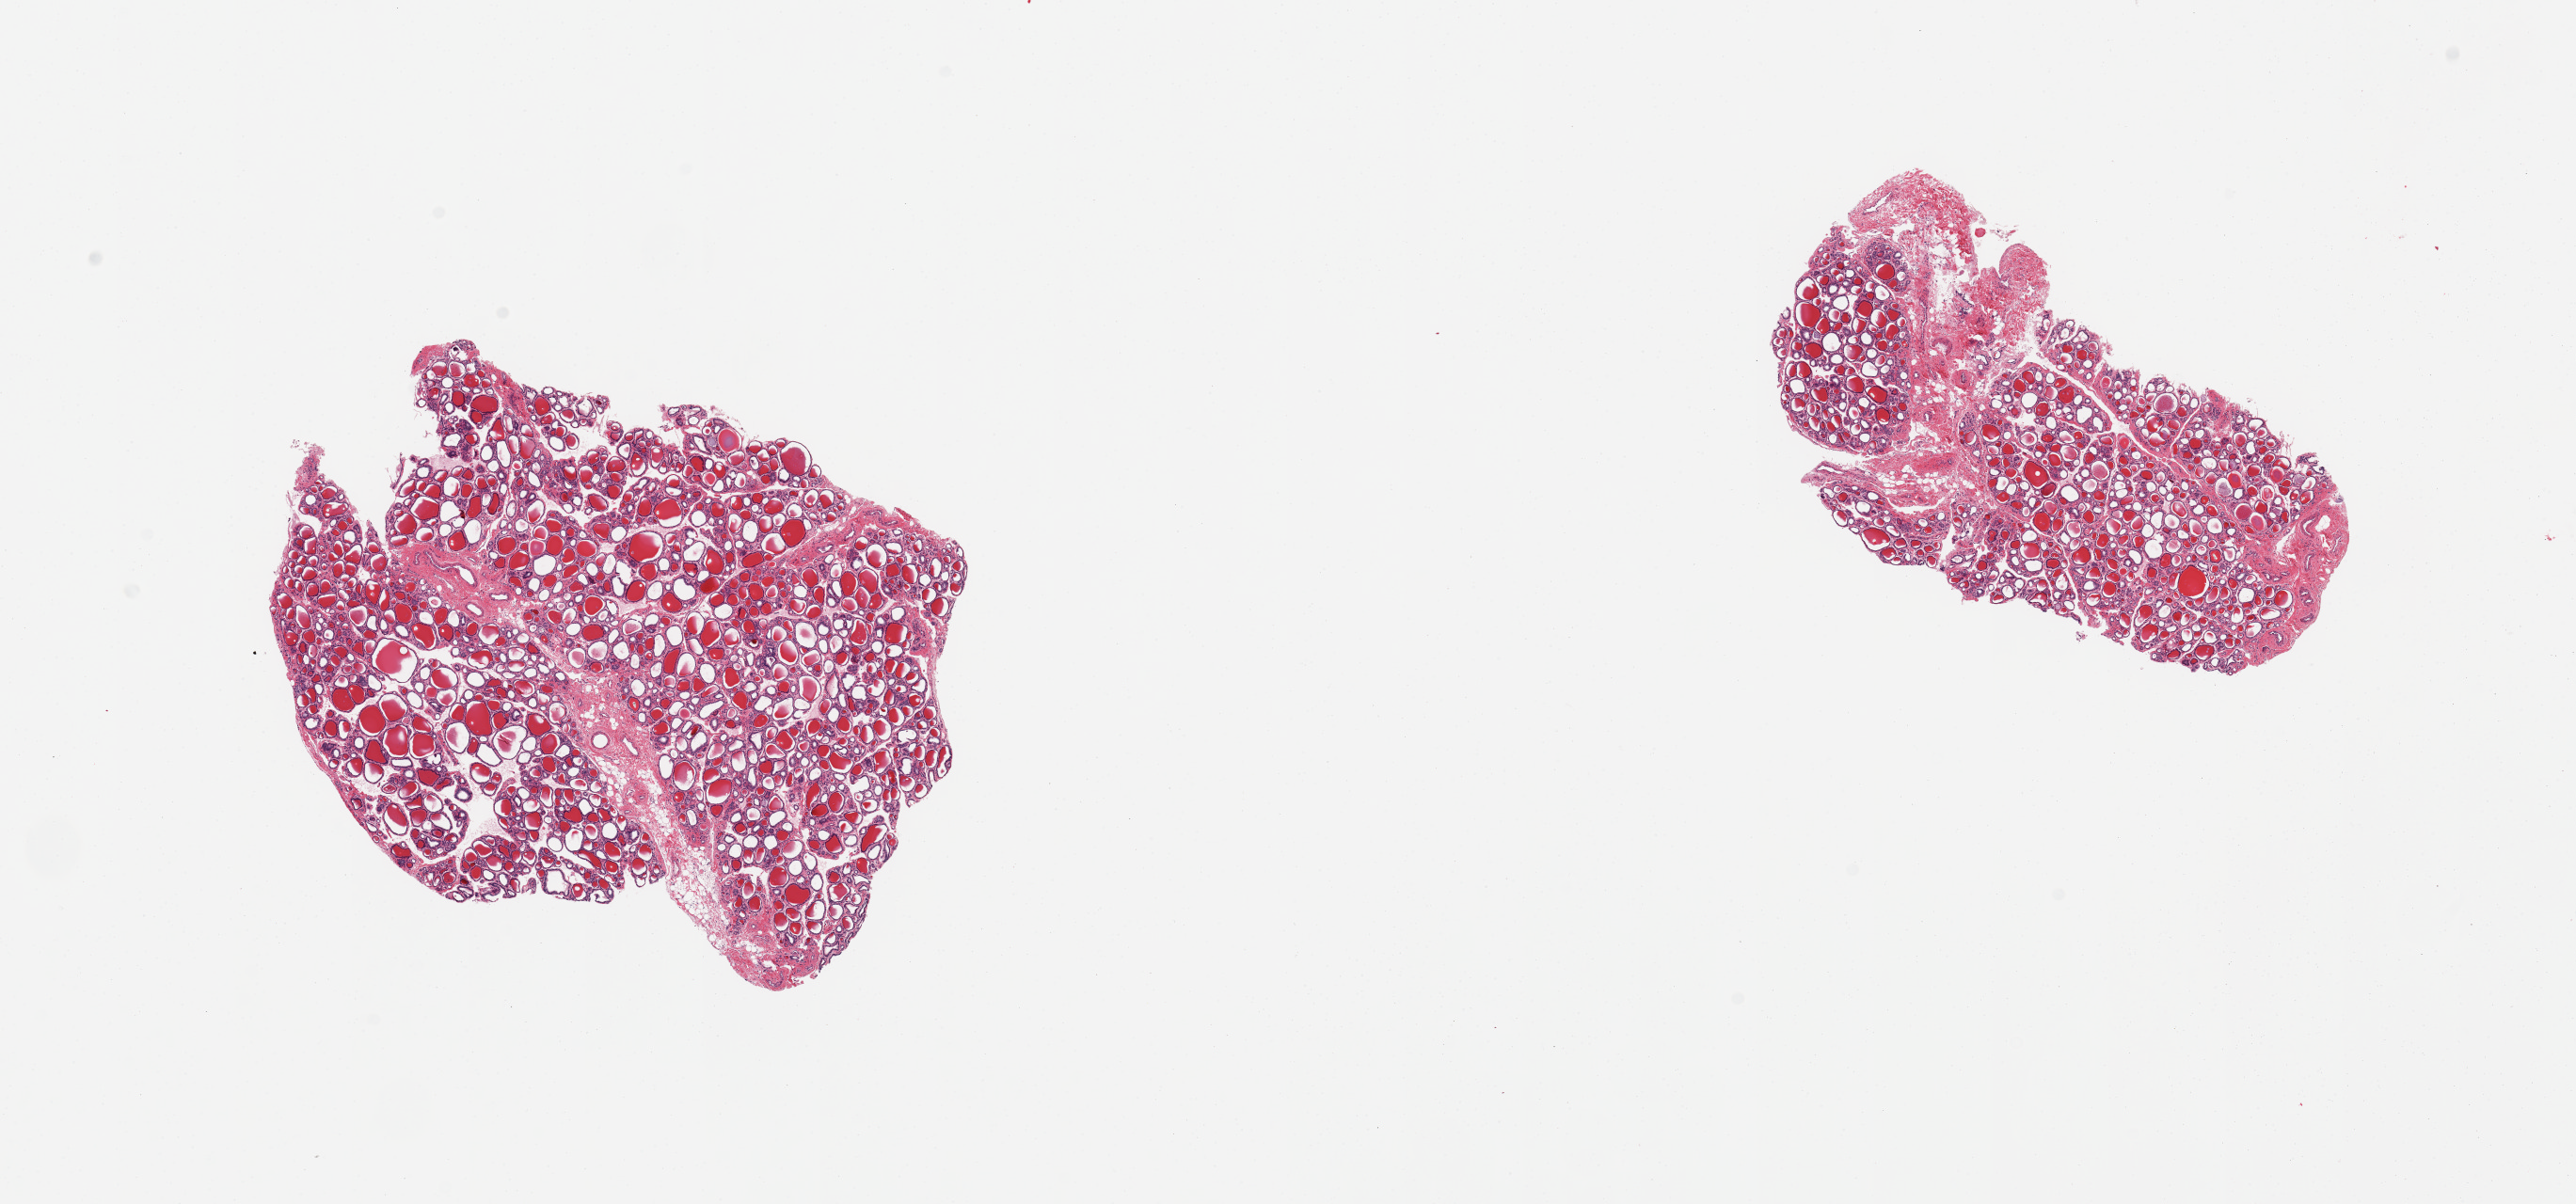
Hematoxylin and eosin (H&E) whole-slide image, brightfield — whole scanned area (about 21.7 x 10.1 mm, from a 20x scan) shown as a low-resolution overview. PAXgene-fixed, paraffin-embedded tissue. Target tissue: thyroid. Tissue donor sample.
Pathologist's review note for this sample: 2 pieces; 20 & 10 % fibrovascular stroma.